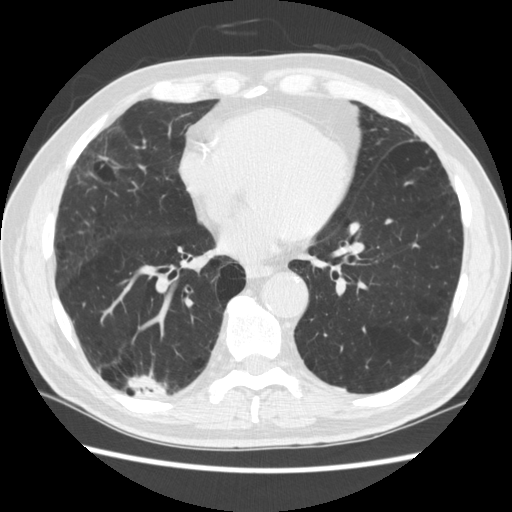
Chest CT (low-dose screening protocol), one axial image; third screening round (two years after baseline); lung window (W 1500 / L -600 HU); 1.25 mm slice thickness; 120 kVp. Male, age 70 years at enrolment. Former smoker at enrolment.
- Lesion marked by an expert reader, bounding box <126,360,180,416> (left, top, right, bottom; pixels).
- The screening reader recorded 4 non-calcified nodules or masses ≥4 mm on this exam (right lower lobe, right lower lobe, left lower lobe, left lower lobe); which of them this box marks is not recorded.
- Official screen result: positive, other.
- Later outcome: lung cancer diagnosed 253 days after this screen — squamous cell carcinoma, NOS, right upper lobe, poorly differentiated (G3), stage IV (AJCC 6th edition).